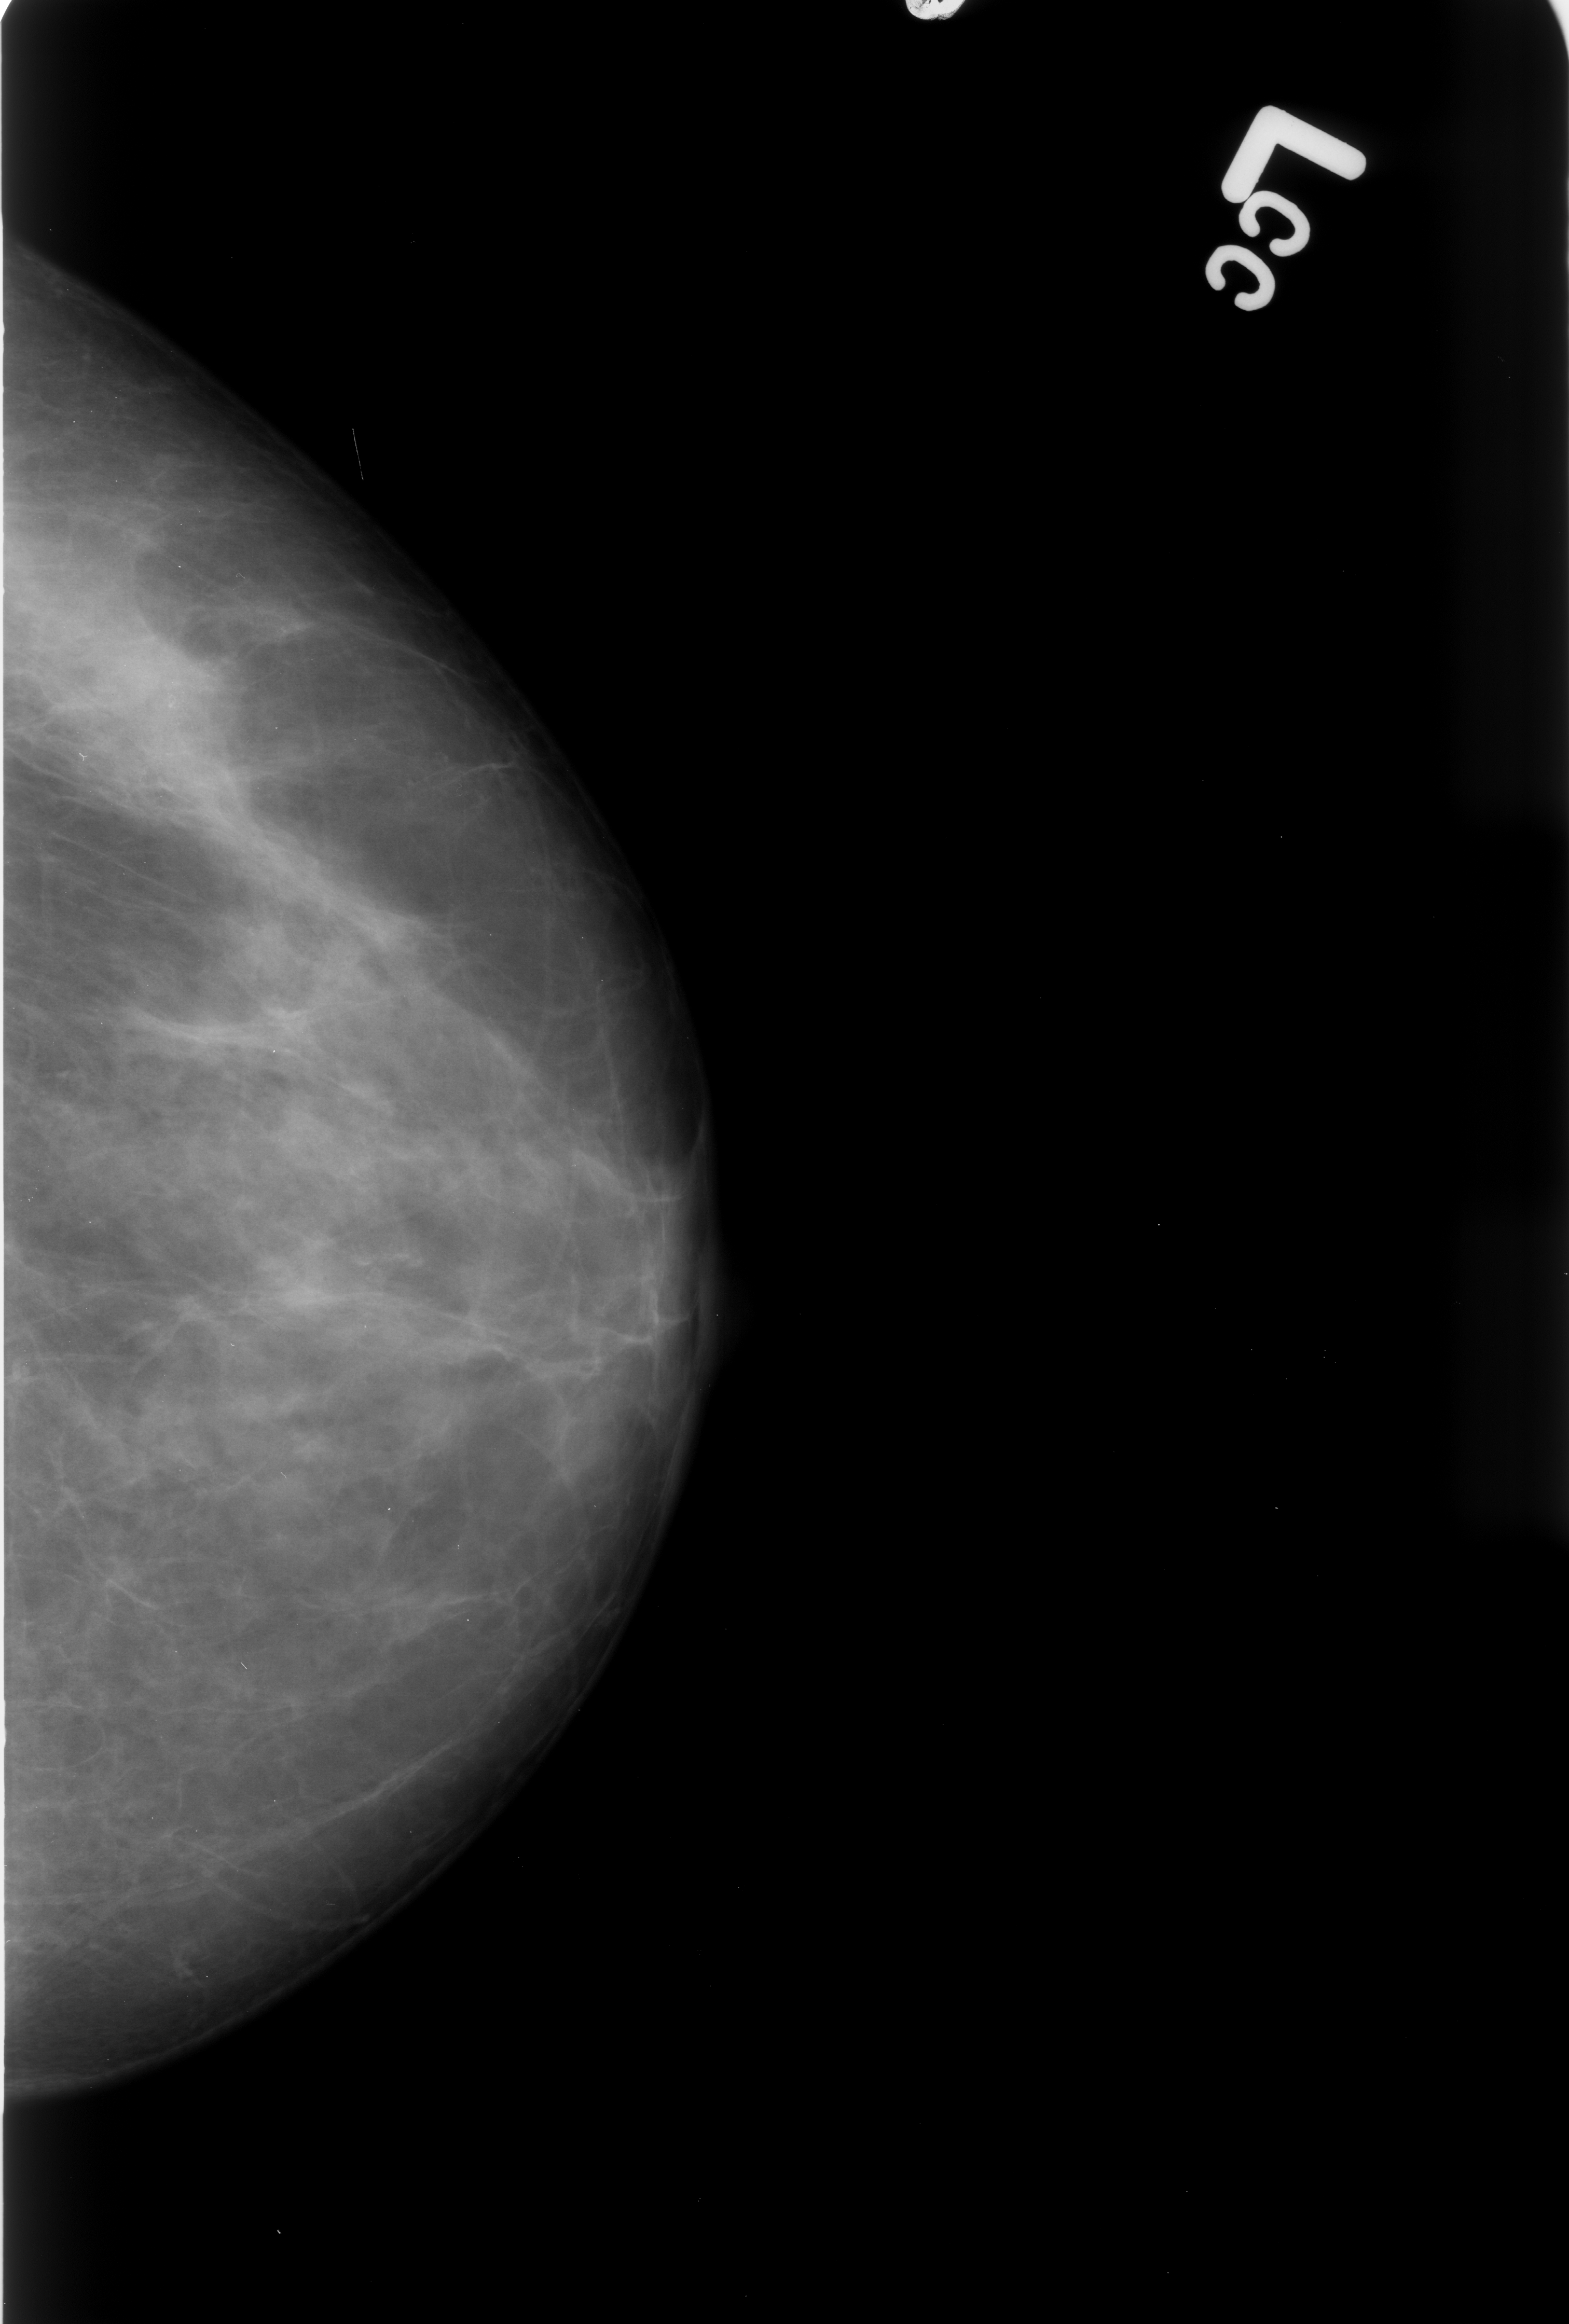
Mammogram (digitized film). Left breast. CC view. Breast composition: scattered fibroglandular densities (BI-RADS density category 2 of 4). 1569 × 2324 image matrix.
Expert-marked regions of interest on this film, with their recorded descriptors:
- calcifications, morphology pleomorphic, distribution clustered; BI-RADS assessment category 4; pathology result (as recorded, not read from the image): benign: bounding box [x1, y1, x2, y2] px = [107, 630, 233, 765]